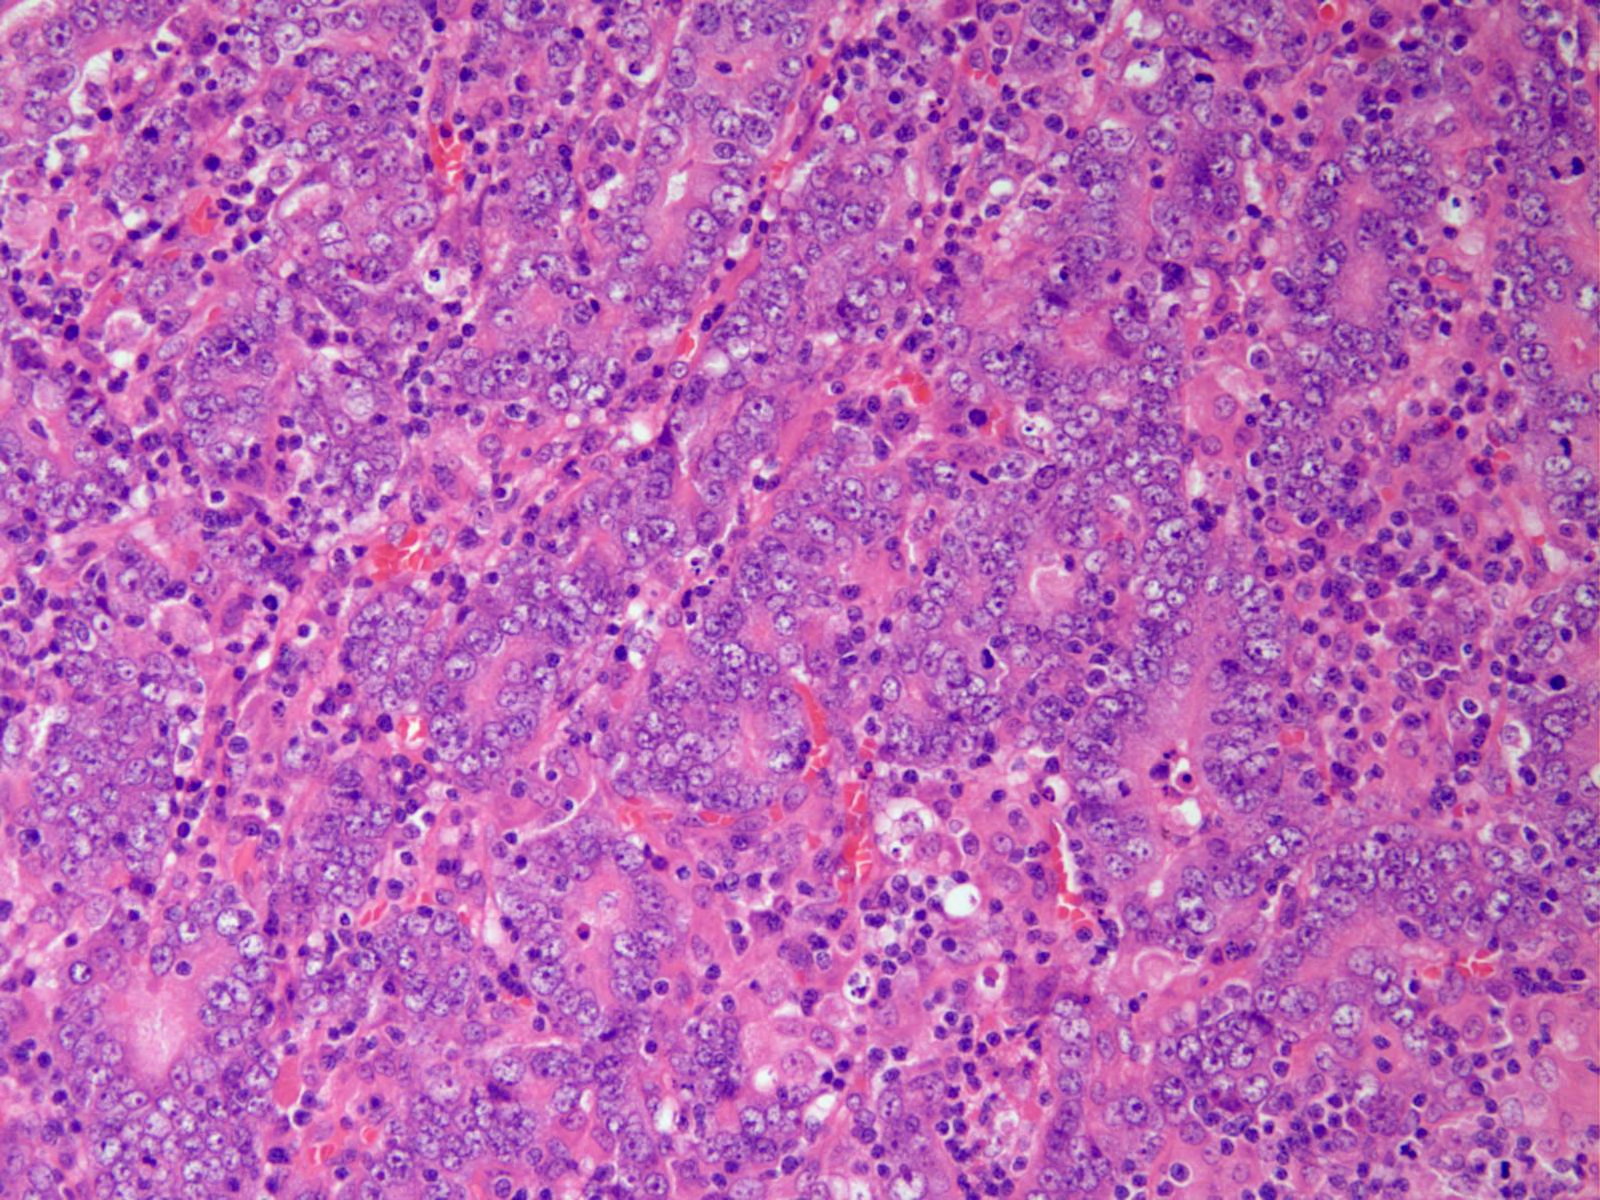
Hematoxylin and eosin (H&E) stained image of one small field of the section, roughly 0.8 x 0.6 mm in extent. Formalin-fixed paraffin-embedded (FFPE) diagnostic section. Primary tumour sample from the stomach. Female, age 80 years at initial diagnosis. Histologic grade: G3 (poorly differentiated).
AJCC pathologic stage: IIIA (6th edition). Lymph nodes positive (case pathology): 3 of 8 examined. Diagnosis: Adenocarcinoma, NOS (body of stomach).